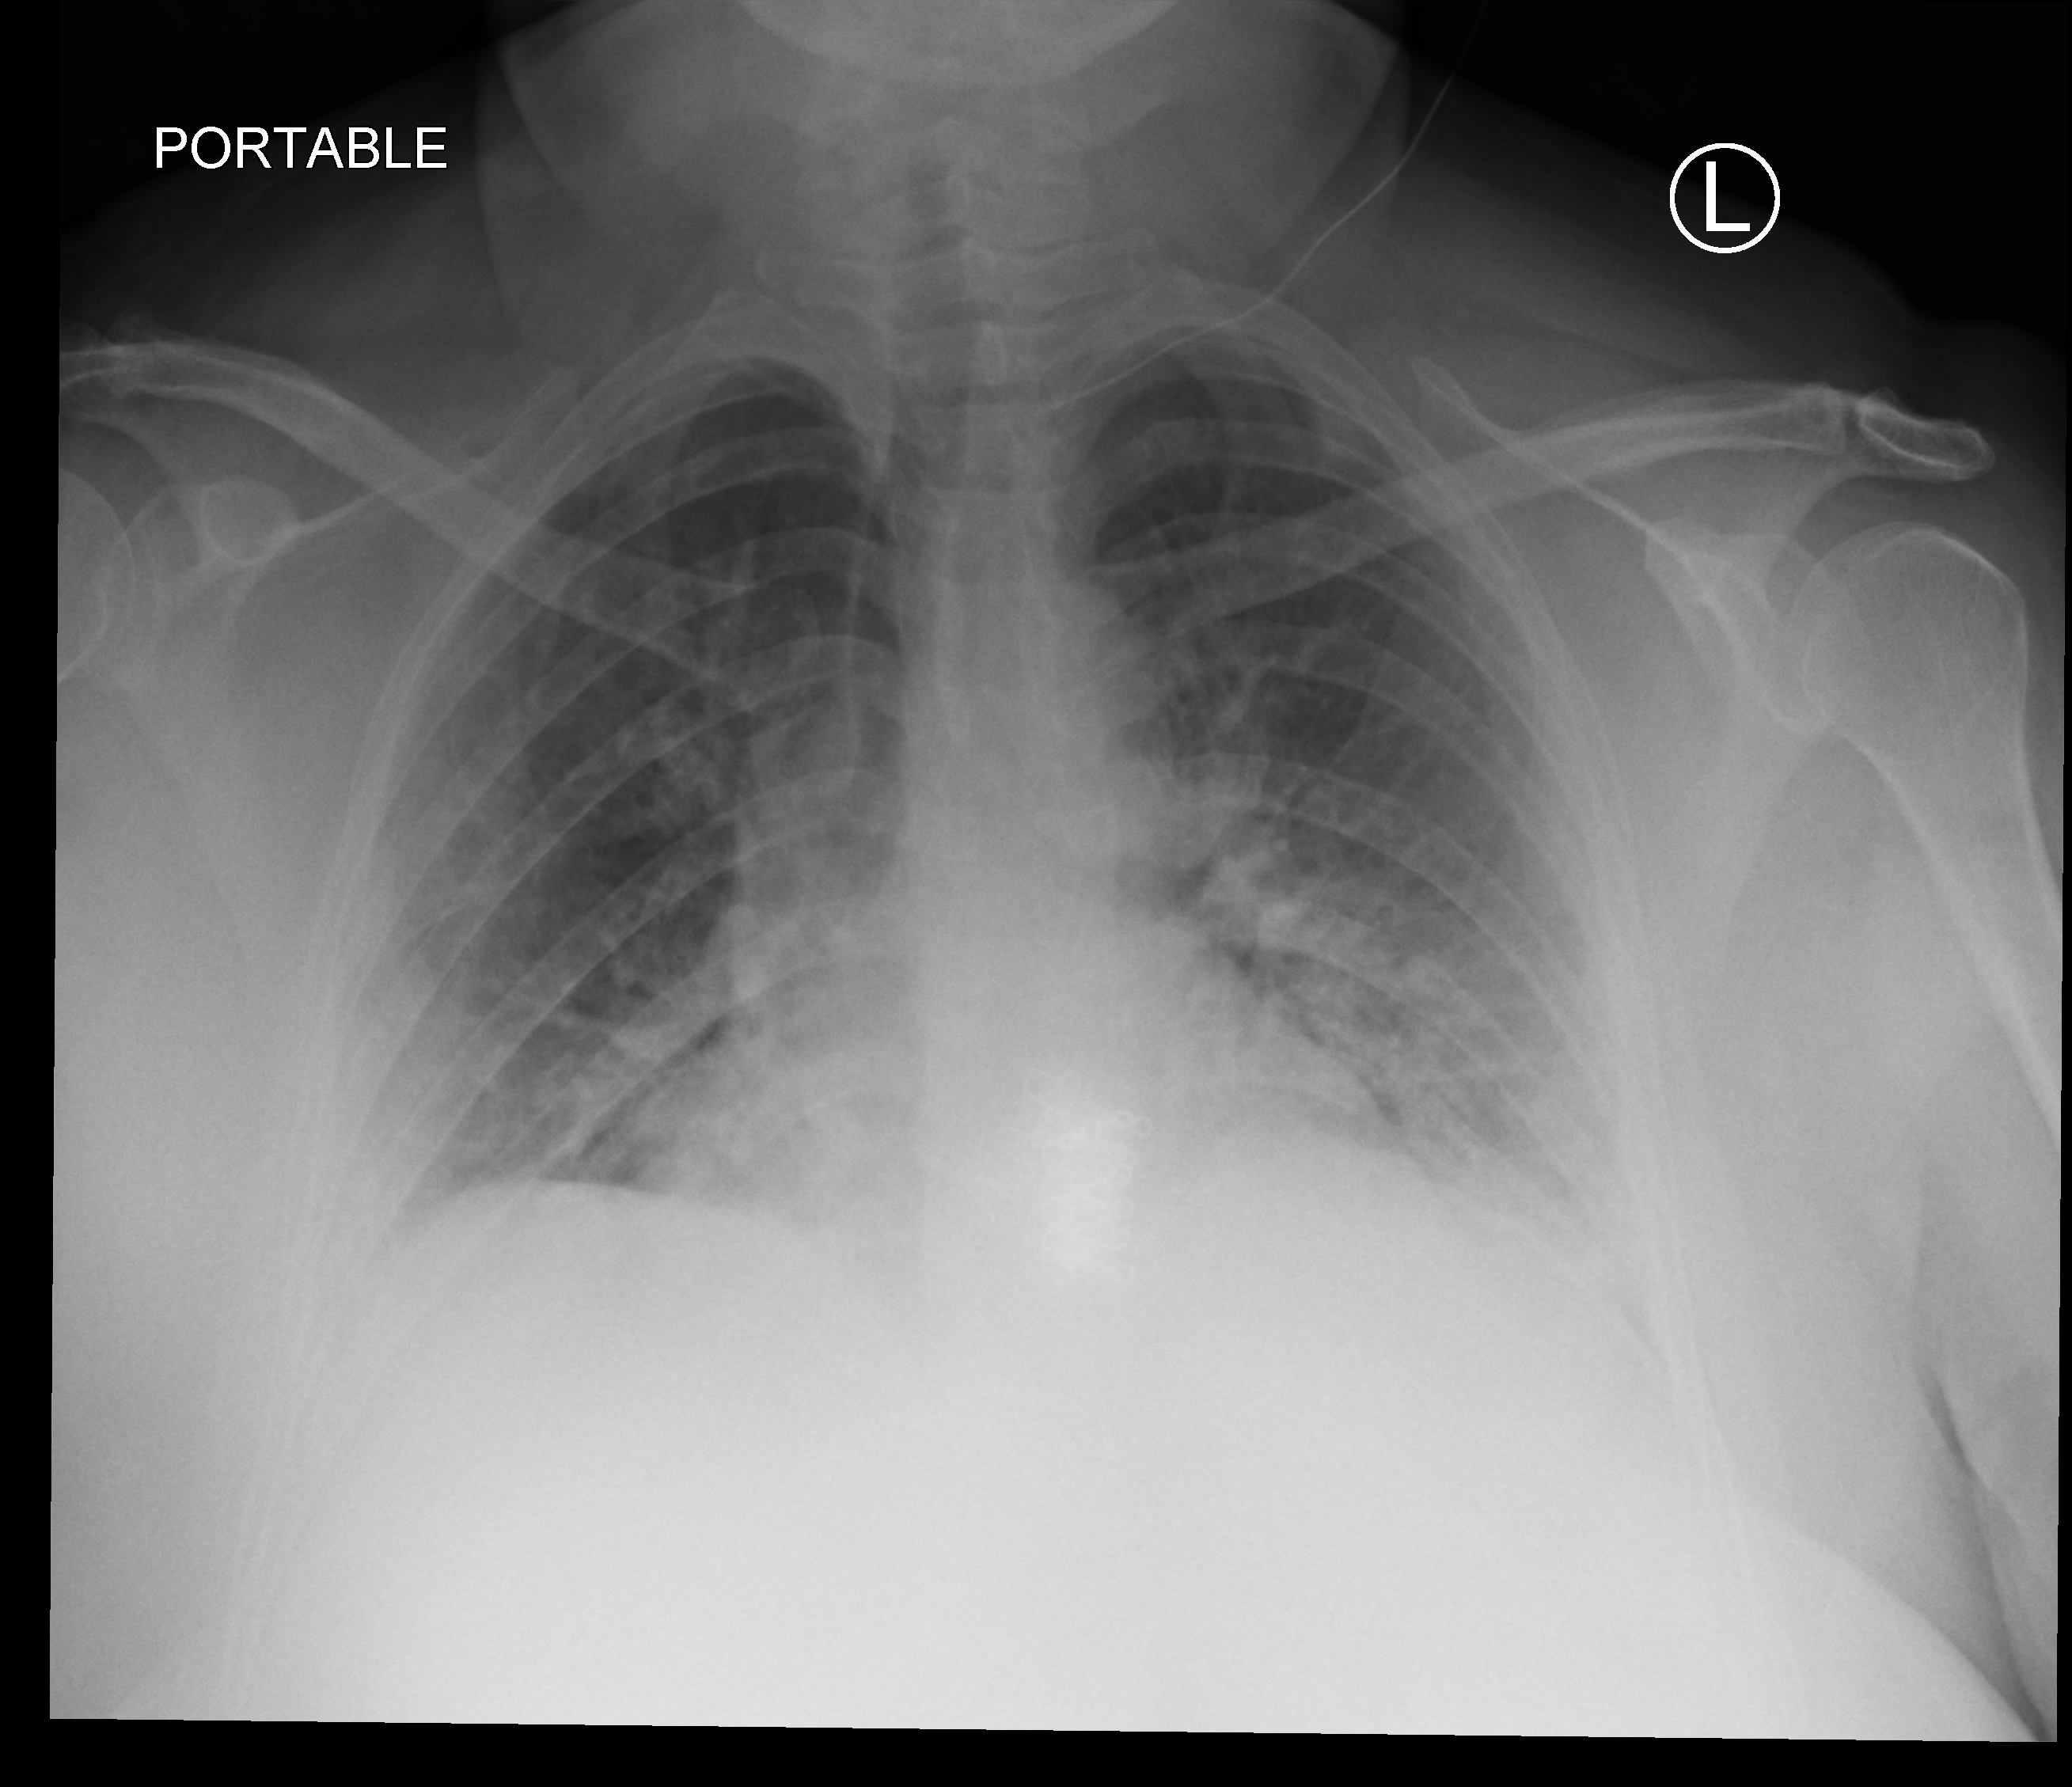
Chest X-ray (portable), anteroposterior (AP) projection. Patient hospitalised with COVID-19; female, aged 18–59 years.
Hospital-stay facts (about this admission, not read from this image; timing relative to this image not recorded):
- mechanically ventilated during this hospital stay: no
- admitted to intensive care during this hospital stay: no